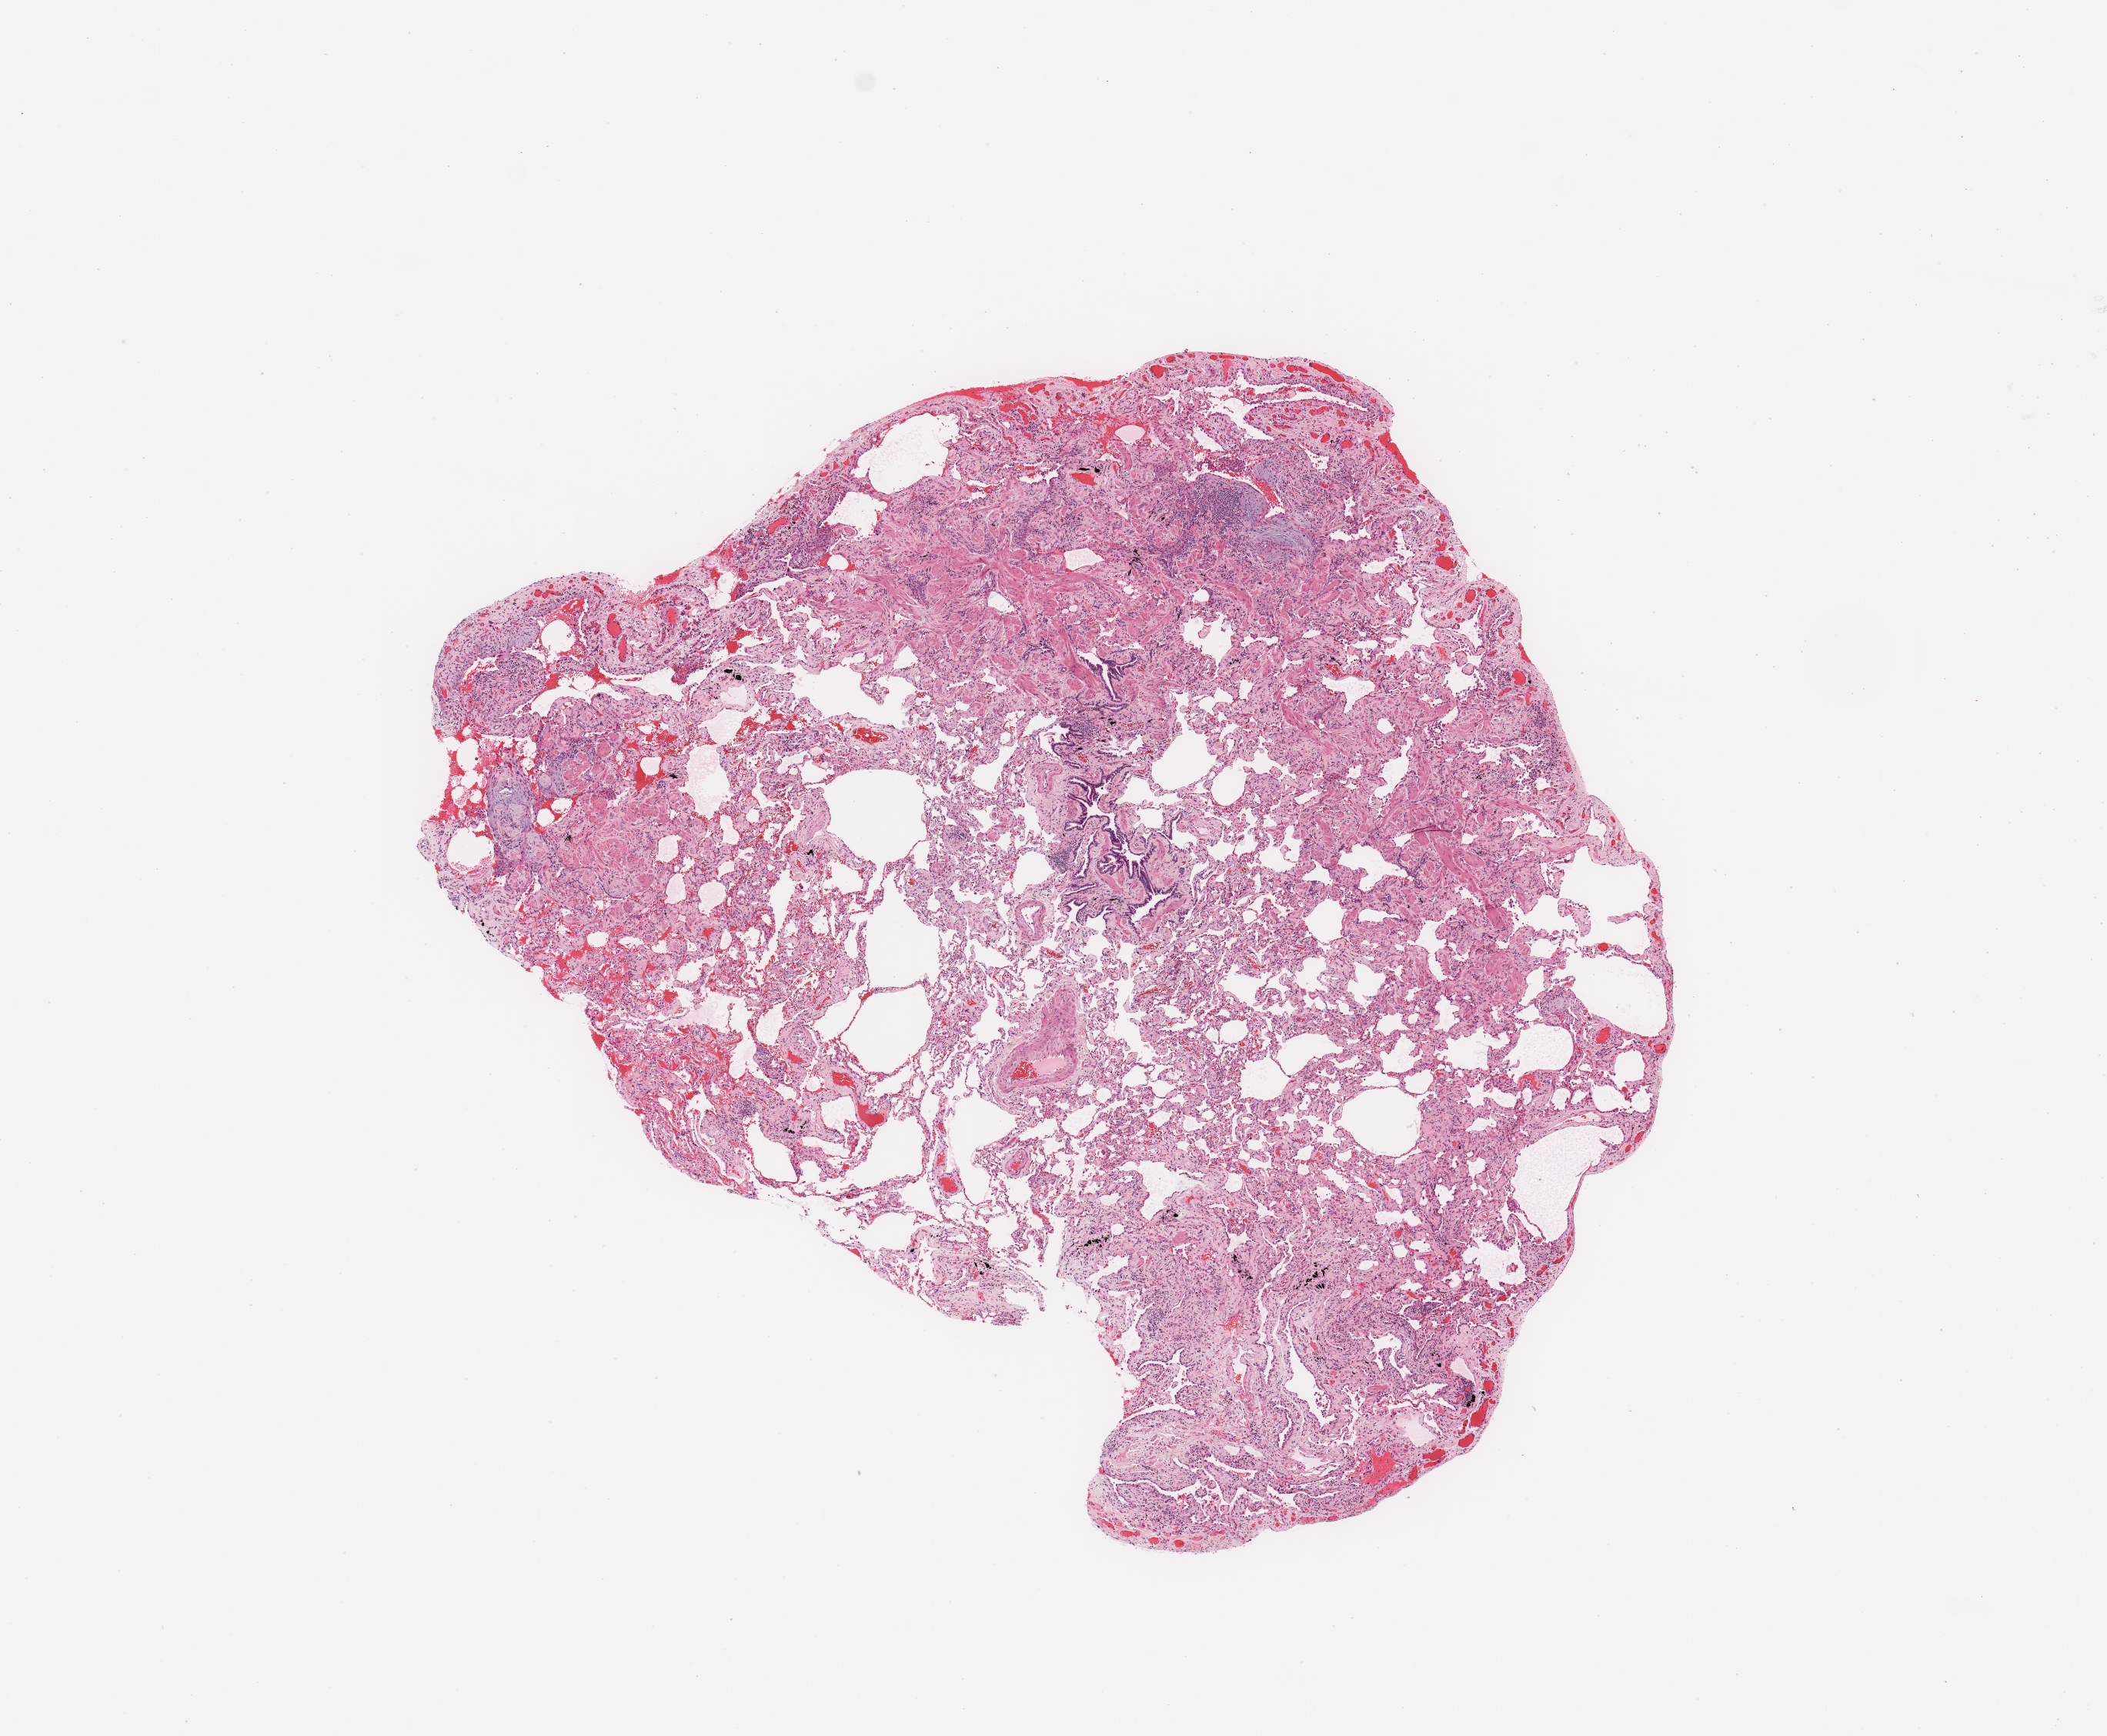
Digitized H&E-stained tissue section (whole slide), shown as a low-resolution overview of the whole scanned area (about 10.8 x 8.9 mm, acquisition: 20x scan); normal (non-tumour) tissue sample, sampled site: lung. Patient: female, age 71 years.
This section: normal (non-tumour) tissue from the same patient. Patient diagnosis: Squamous cell carcinoma, NOS.